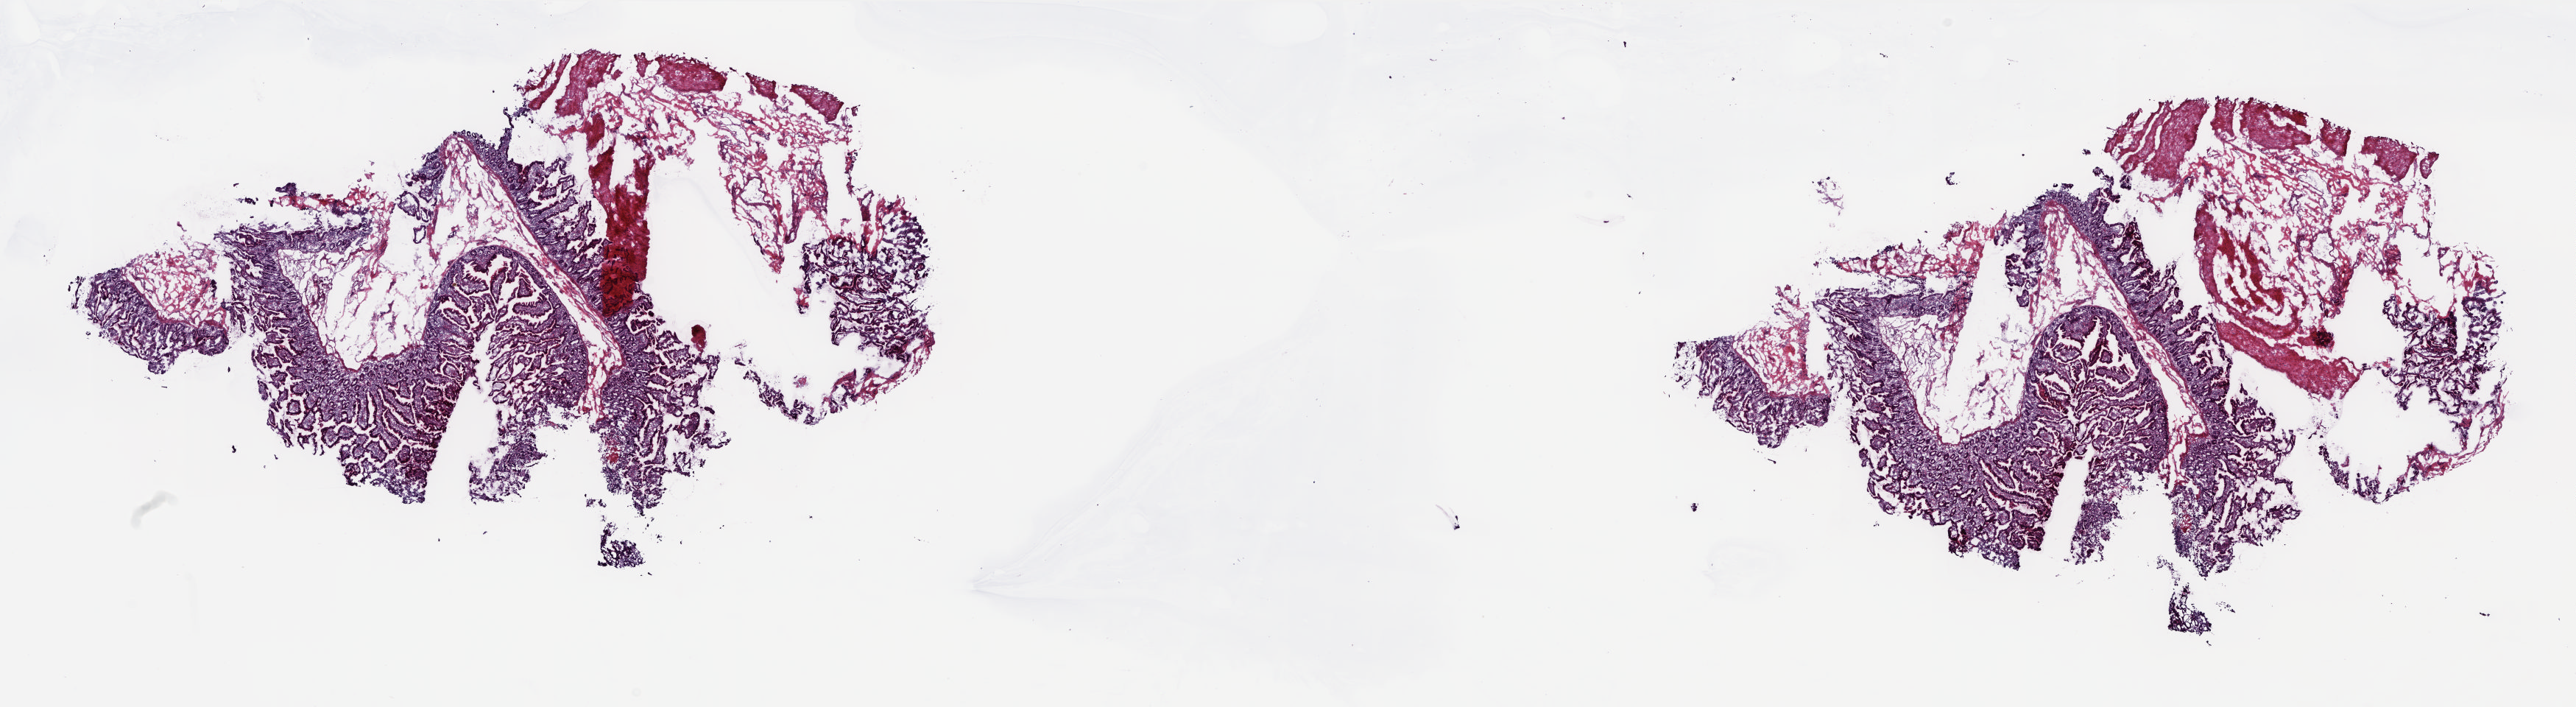
H&E whole-slide image — low-resolution overview of the scanned area, about 27.9 x 7.7 mm (acquisition: 20x scan), frozen section from the top of the tissue portion, sample: solid tissue normal (non-tumour tissue), pancreas. Male patient; age at initial diagnosis 56 years. Pathologist review of this section (percent, as recorded): tumour cells 0%, tumour nuclei 0%, normal cells 100%, stromal cells 0%, necrosis 0%. Inflammatory infiltration, as recorded: lymphocyte infiltration 5%, monocyte infiltration 0%, neutrophil infiltration 0%.
This section: solid tissue normal sample (biorepository sample class). Patient diagnosis: Infiltrating duct carcinoma, NOS (head of pancreas).